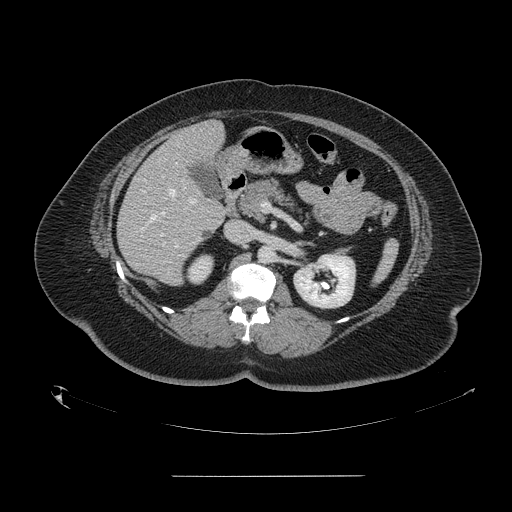
Contrast-enhanced abdominal CT, one axial slice; position 76 of 164 along the scan axis; 120 kVp; intravenous contrast given; soft-tissue window (W 400 / L 40 HU); 512 × 512 image matrix, field of view 495 × 495 mm. Female patient, age 52 years. From the clinical record (not read from this slice): diagnosis: colorectal cancer liver metastases, imaged before liver resection; multiple liver metastases: yes; largest metastasis: 3.5 cm; chemotherapy before resection: no.
Annotated regions visible in this slice (manually delineated by an expert):
- hepatic veins: bounding box (x1, y1, x2, y2) in pixels: (141, 189, 188, 229)
- liver: (118, 122, 226, 285)
- planned liver remnant (the part of the liver to remain after resection): (177, 122, 224, 165)
- portal vein (with intrahepatic branches): (161, 176, 195, 236)
- liver metastasis: (203, 231, 210, 237)